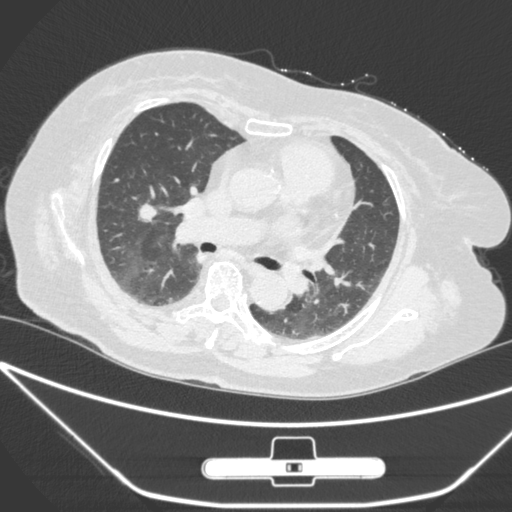
Chest CT, one axial slice; 120 kVp; lung window (W 1500 / L -600 HU); 1 mm slice thickness; 512 × 512 image matrix. Patient: female, 65 years. Case-level facts recorded for this patient, not image findings: clinical TNM (as recorded): T1c N0 M0.
Structures marked on this image (rectangle marked by the reading radiologist):
- lung tumour (recorded histology: adenocarcinoma): box from (x=136, y=195) to (x=167, y=236) px